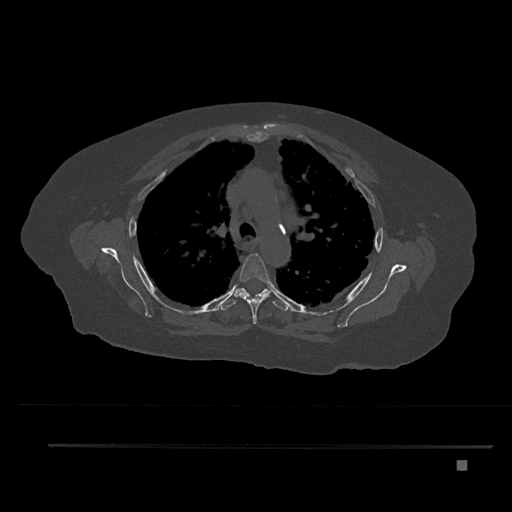
CT including the spine, one axial slice; slice 590 of 797 in the series (ordered by position); reconstruction kernel Br40s/3; 120 kVp; bone window (W 1800 / L 400 HU); 512 × 512 image matrix. Patient: female, 76 years. Case-level facts recorded for this patient, not image findings: primary cancer: lung; vertebrae with lytic lesions (as recorded): T11, L3.
Structures marked on this image (semi-automatically segmented with operator editing):
- T4 vertebra: box from (x=234, y=253) to (x=271, y=324) px
- T5 vertebra: (x=219, y=283)–(x=289, y=311)